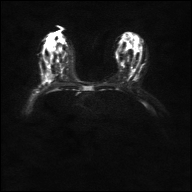
Breast MRI, one axial slice. Diffusion-weighted series; image 2 of 4 stored at this slice position (different b-values; order by instance number). 1.5 T. 4 mm slice thickness. 192 × 192 image matrix, field of view 360 × 360 mm. Female patient.
Outlined on this slice (outlined manually by an expert reader):
- tumour on diffusion-weighted imaging: bounding box [x1, y1, x2, y2] px = [42, 80, 45, 82]